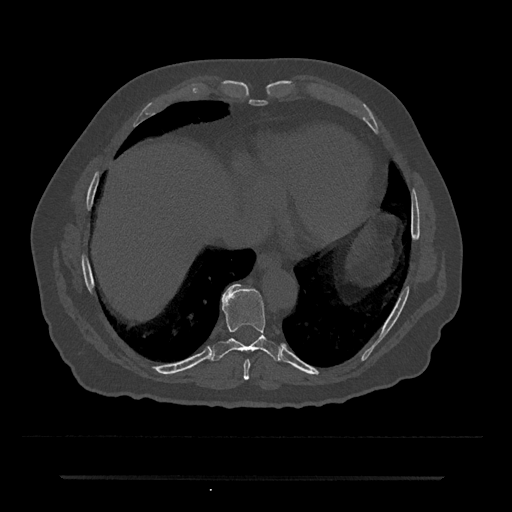
CT including the spine, one axial slice. Slice 284 of 797 in the series (ordered by position). Reconstruction kernel Br40s/3. 120 kVp. Bone window (W 1800 / L 400 HU). 512 × 512 image matrix. Male patient, age 69 years. Case-level facts recorded for this patient, not image findings: primary cancer: prostate.
Annotated regions visible in this slice (semi-automatic segmentation, software-assisted and operator-edited):
- T8 vertebra: bounding box [x1, y1, x2, y2] px = [244, 359, 250, 380]
- T9 vertebra: [212, 284, 282, 362]